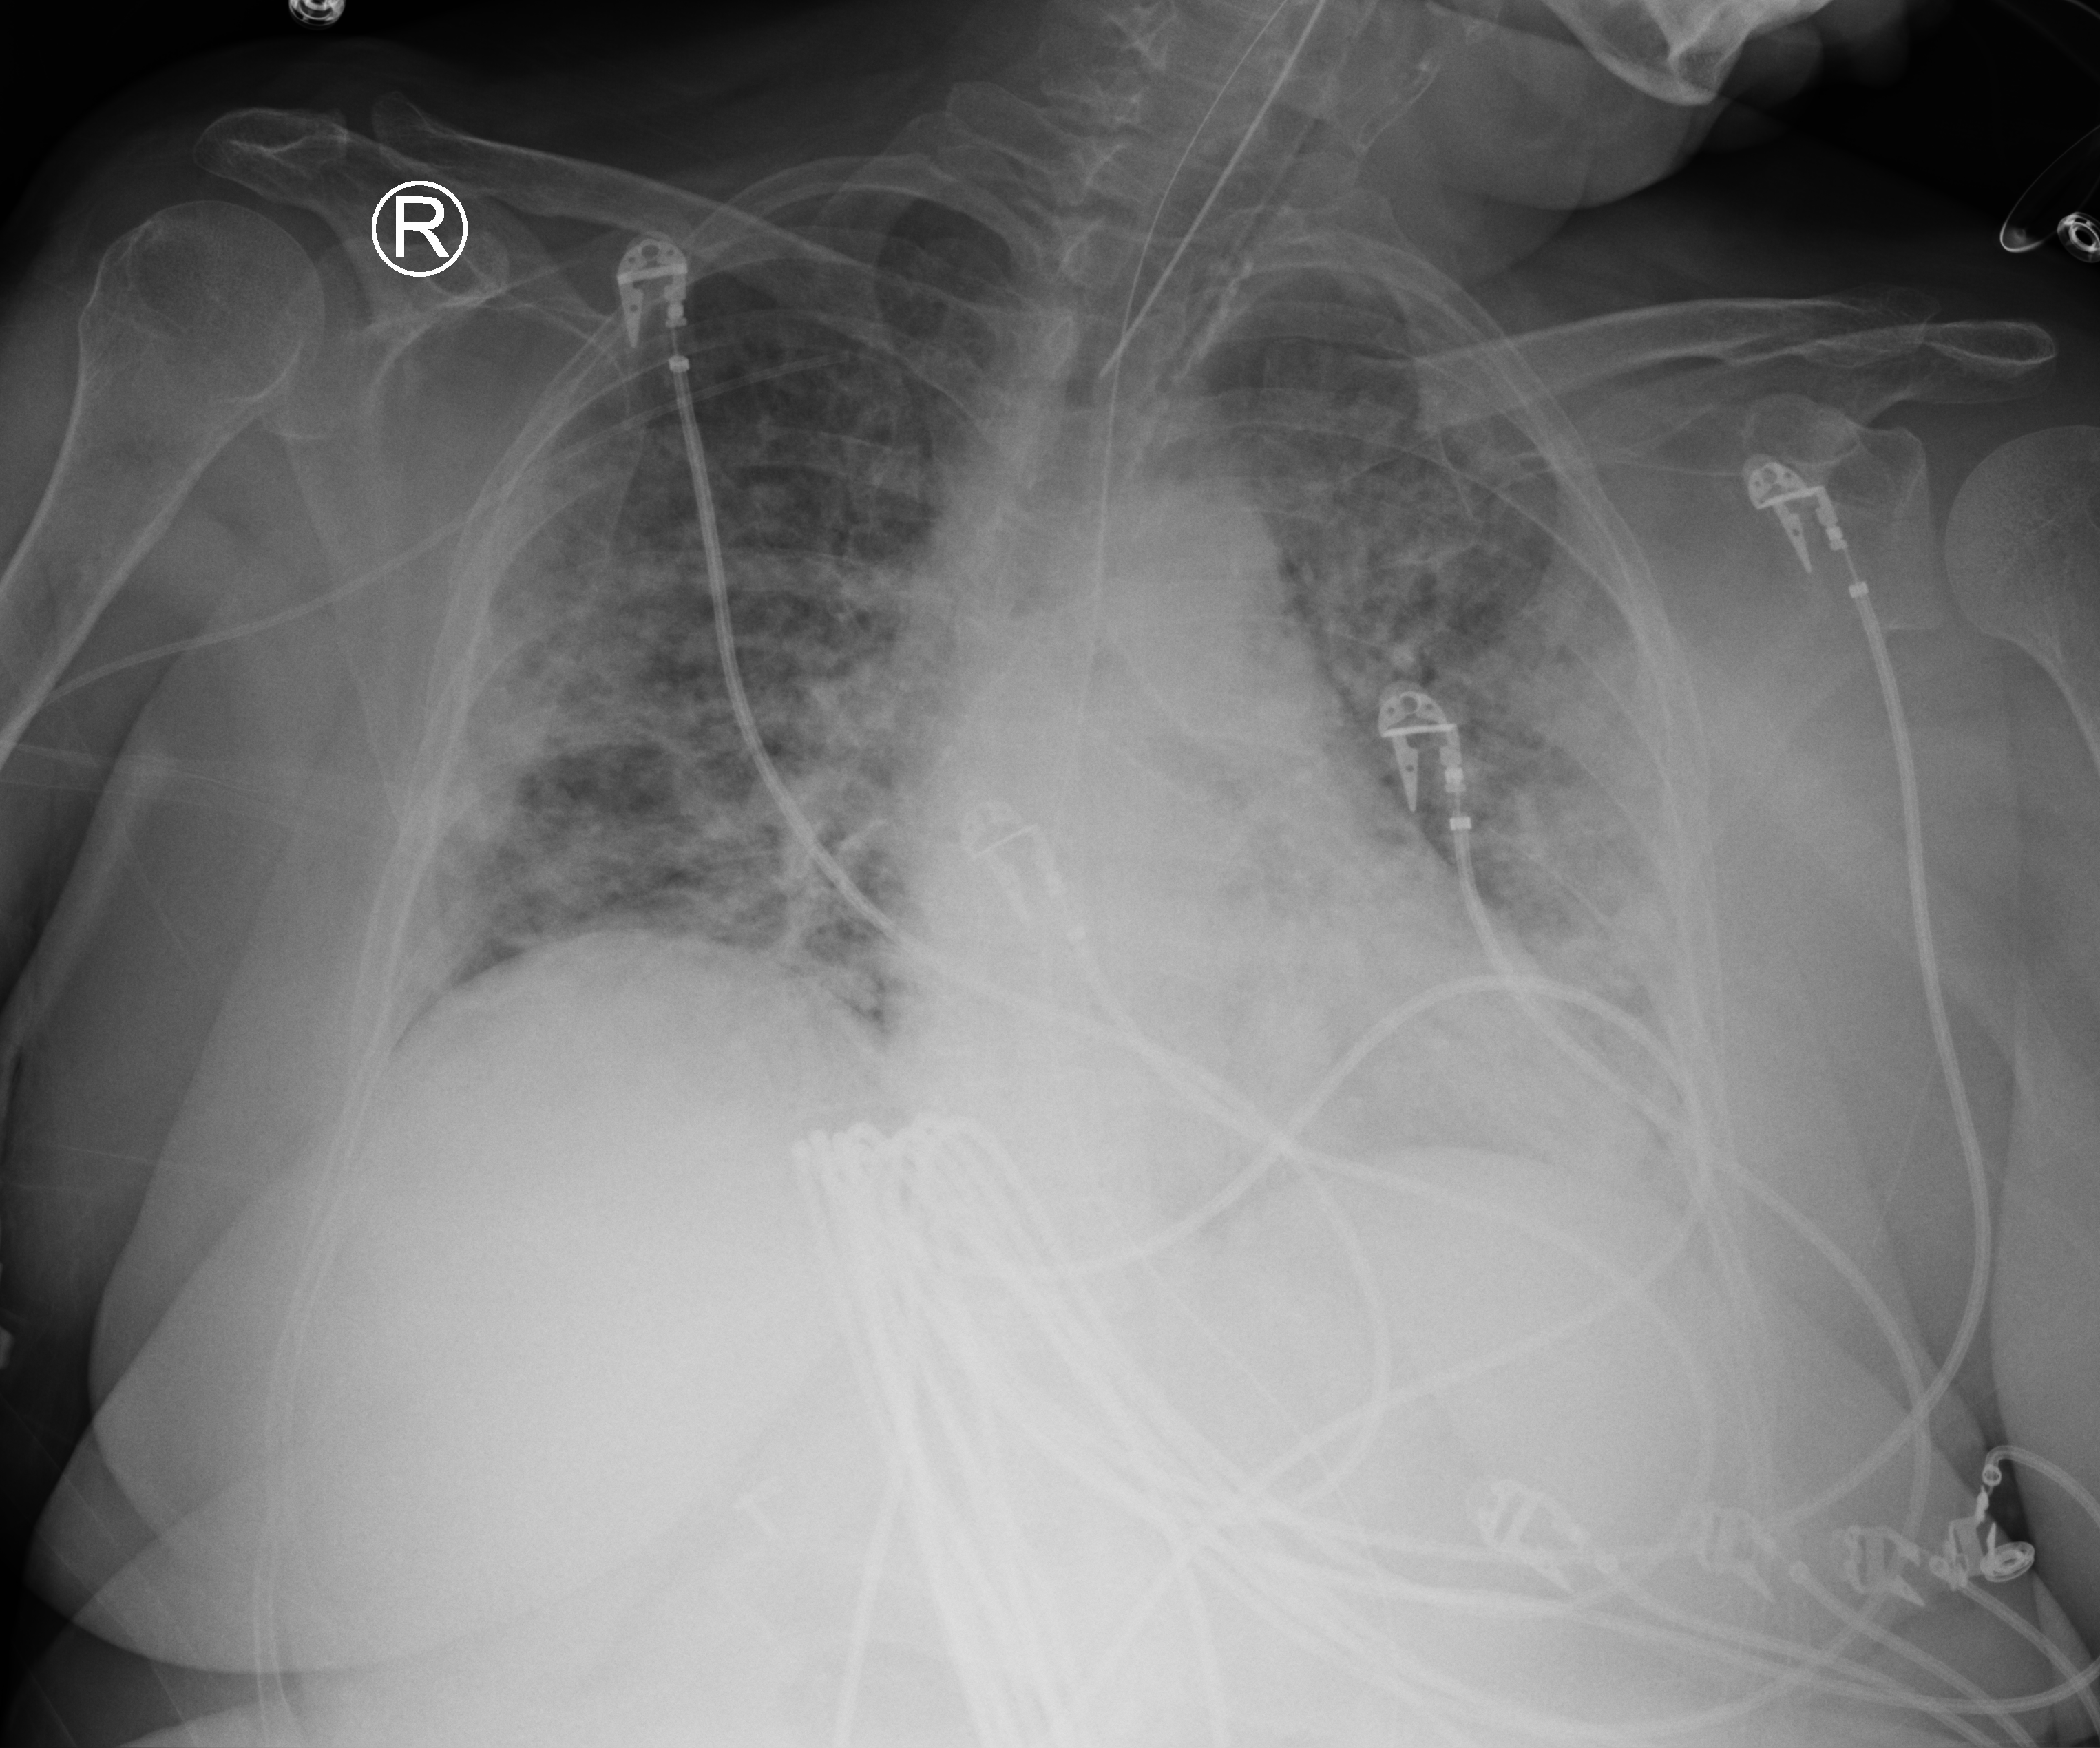
Portable chest radiograph; anteroposterior (AP) projection. Patient hospitalised with COVID-19; female, aged 18–59 years.
Admission-level facts for this patient (not findings on this image; timing relative to this image not recorded): hypertension (admission record): no.